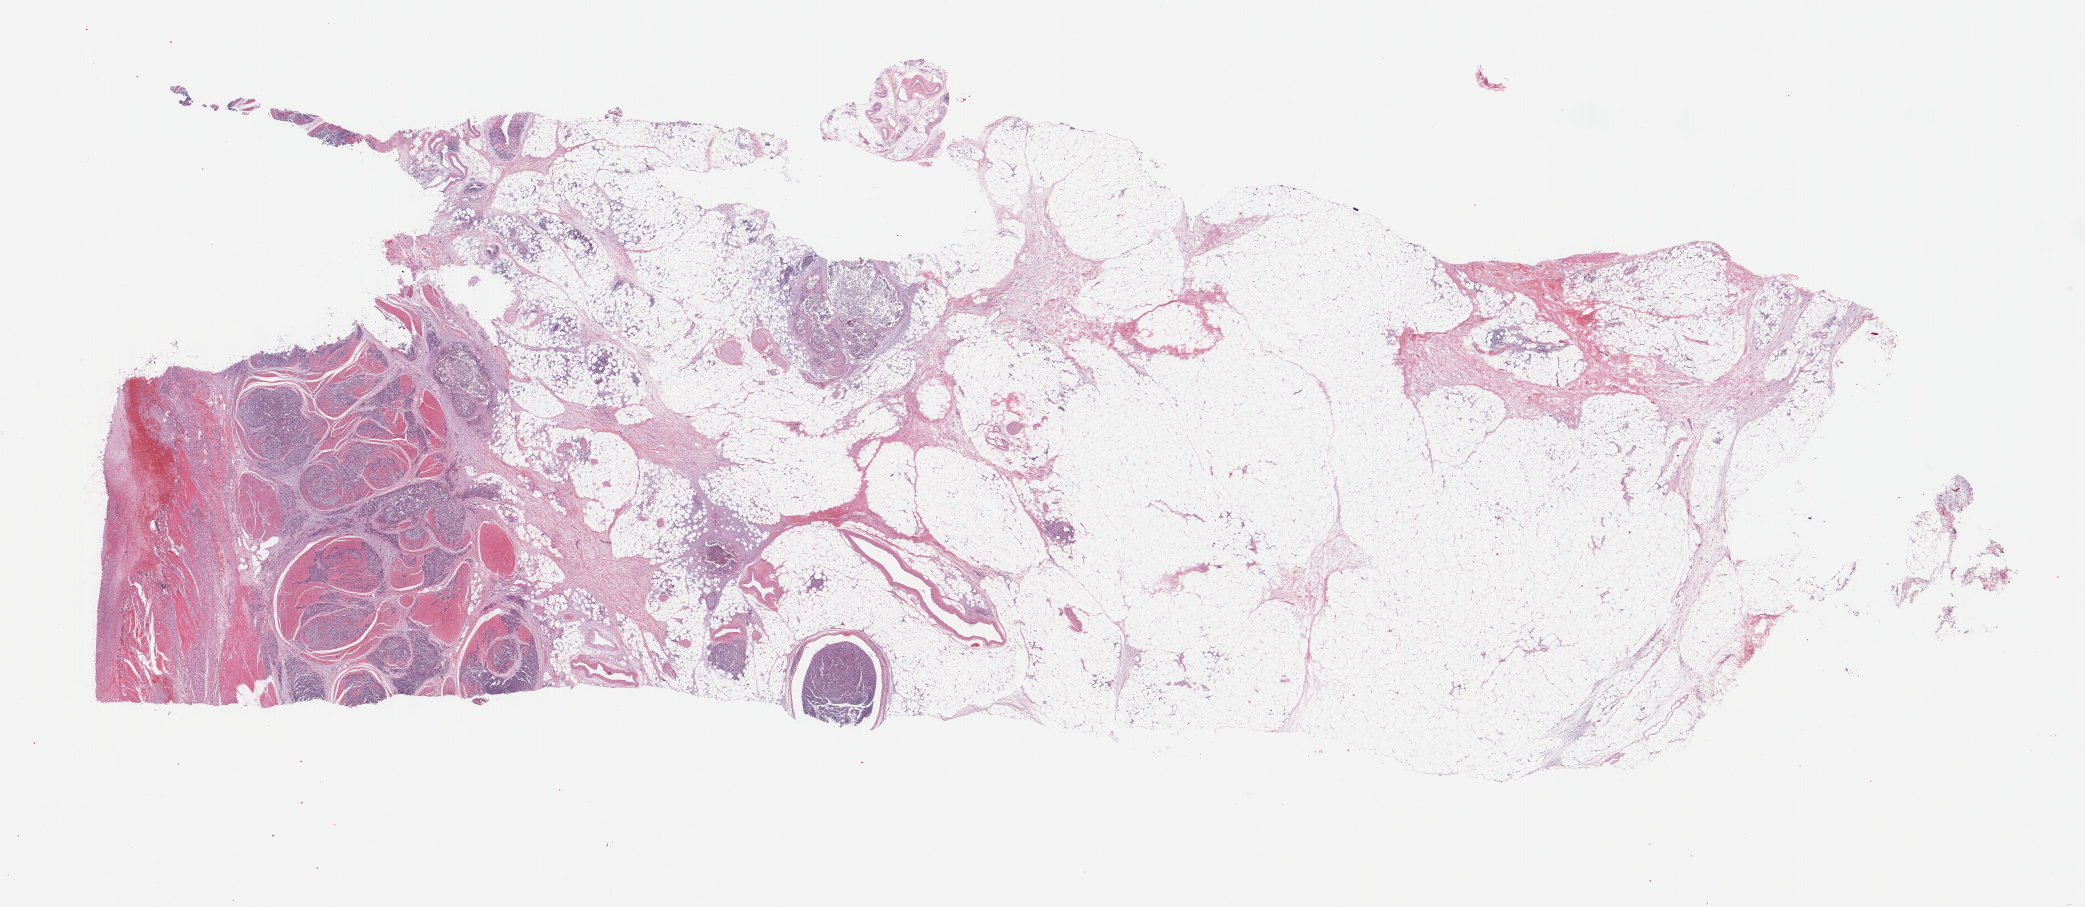
Digitized H&E-stained tissue section (whole slide) — a low-resolution overview of the entire scanned area, about 33.7 x 14.7 mm (acquisition: 40x scan); formalin-fixed paraffin-embedded (FFPE) diagnostic section; bladder, primary tumour sample. Patient: male, age at initial diagnosis 68 years.
Histologic diagnosis: Transitional cell carcinoma.